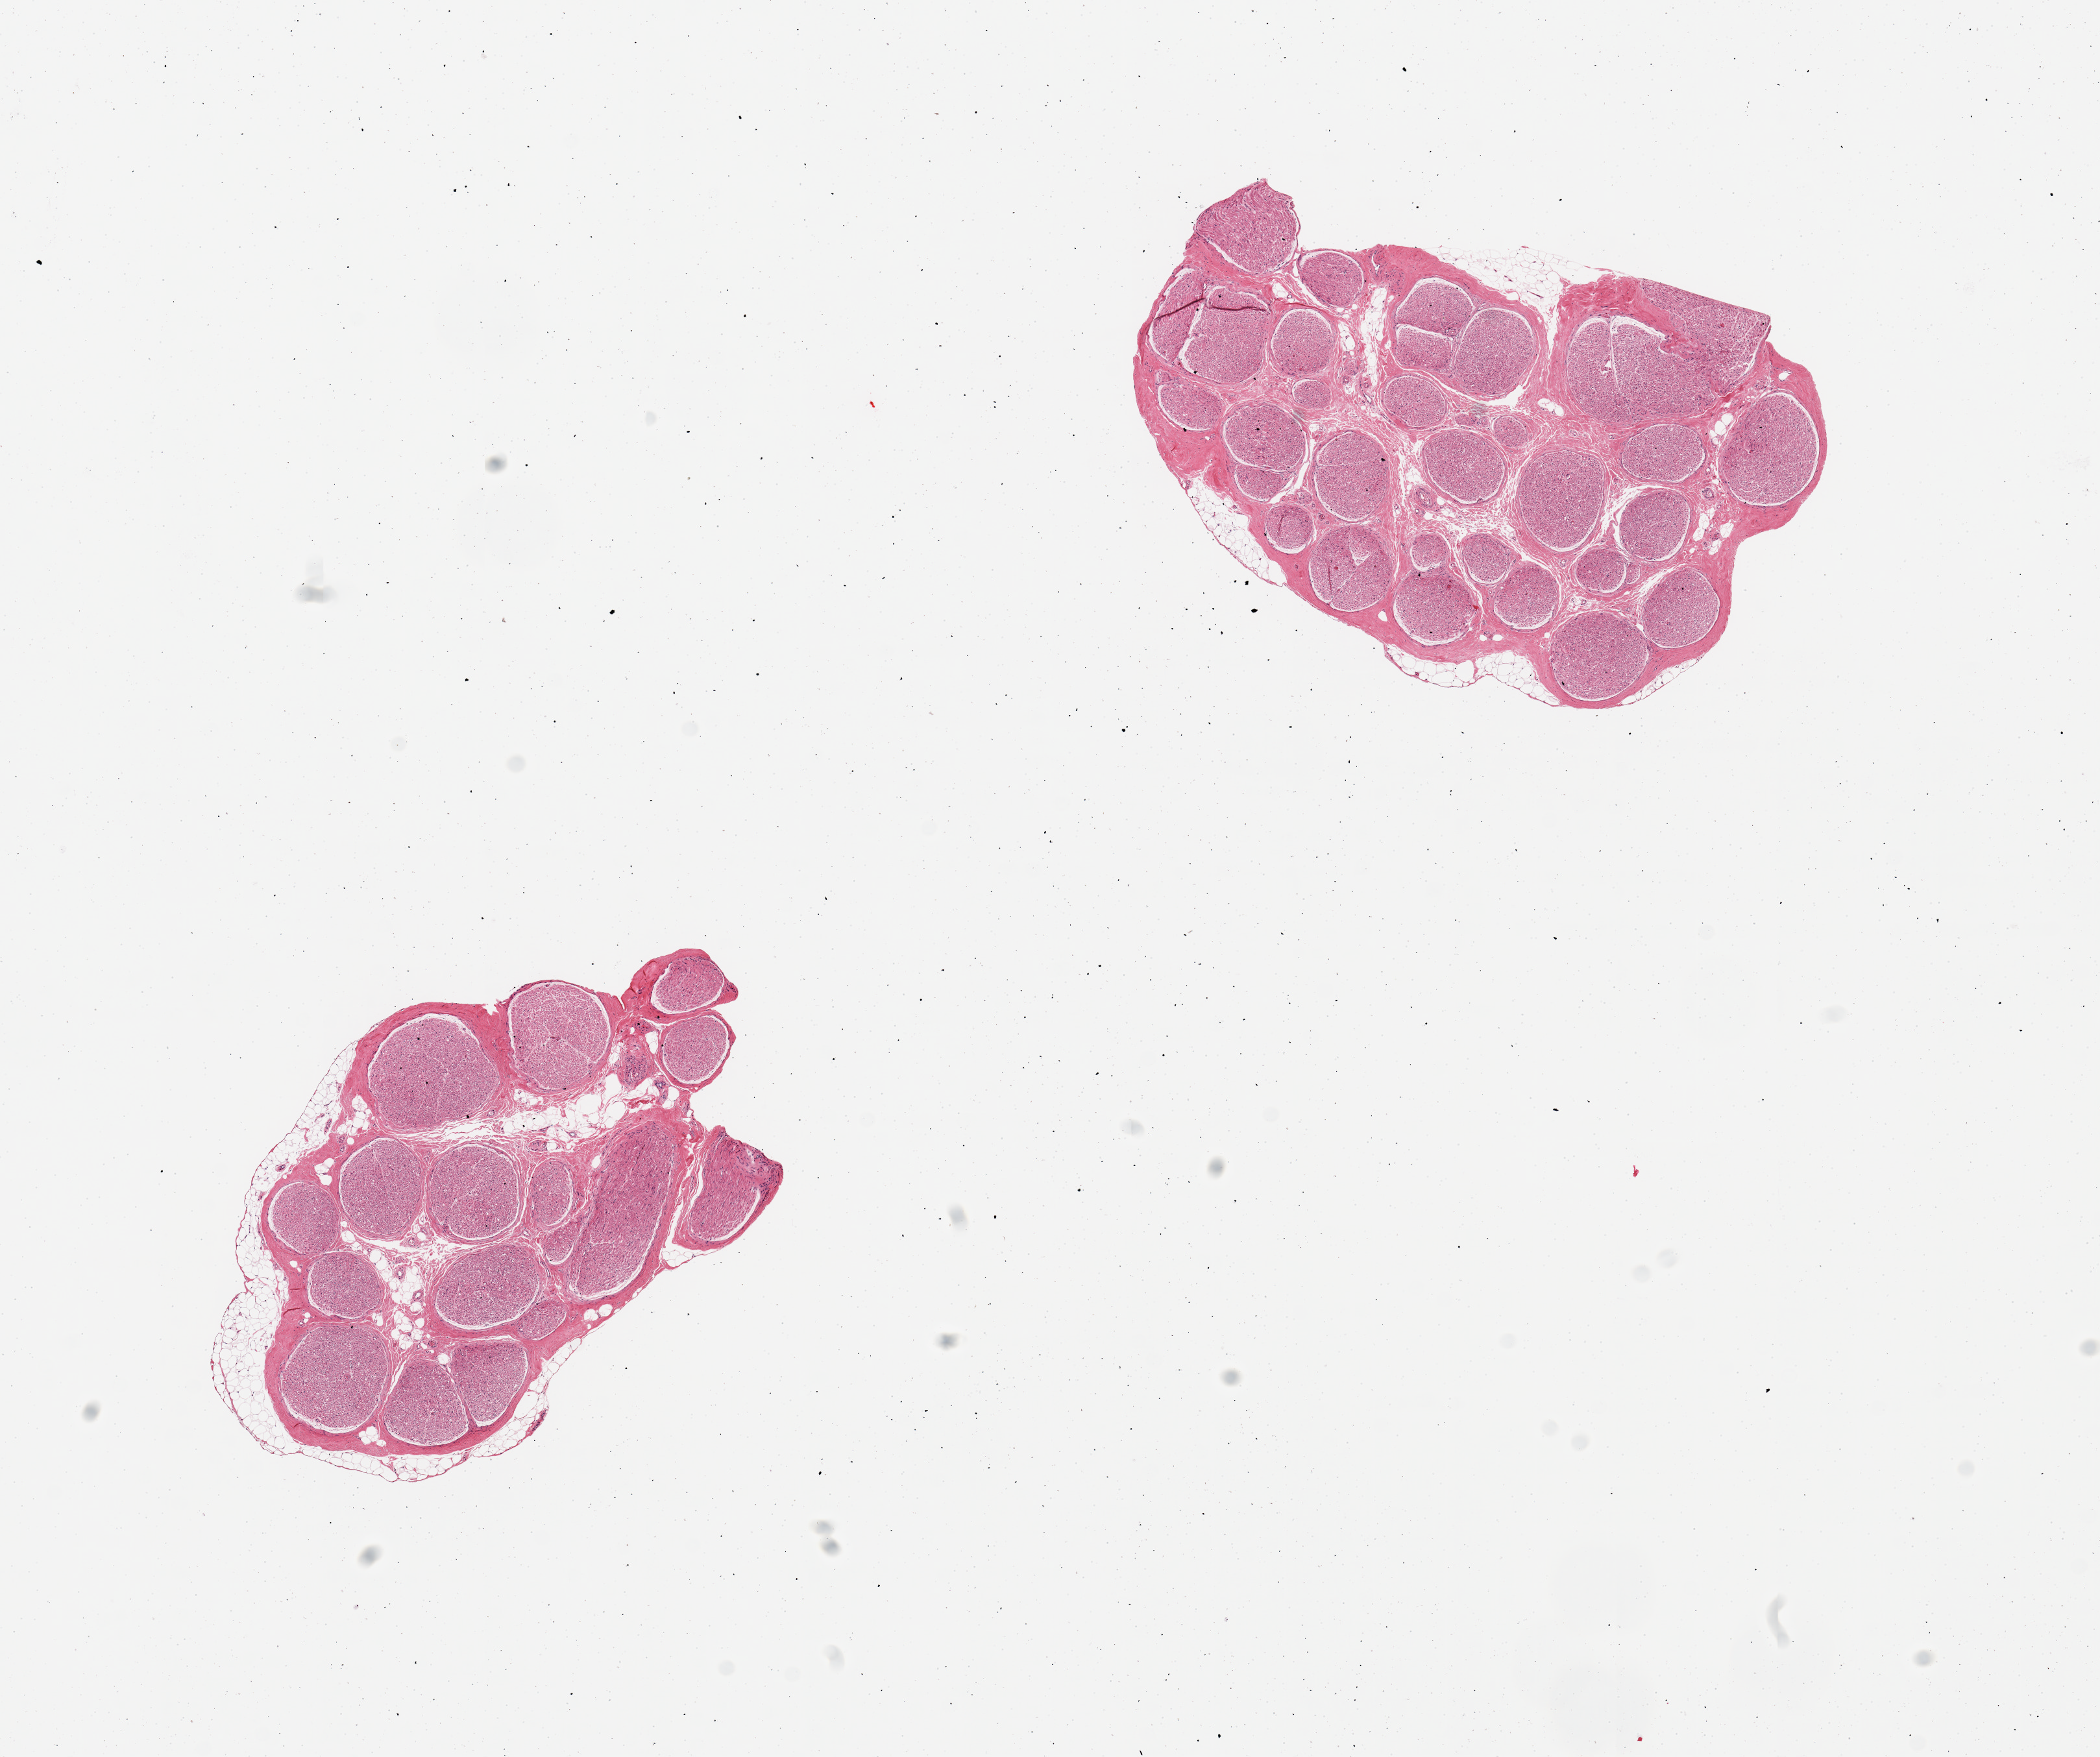
Haematoxylin and eosin whole-slide image — whole scanned area (about 12.8 x 10.7 mm, slide scanned at 20x) shown as a low-resolution overview; PAXgene-fixed paraffin-embedded (PFPE) section; section of tibial nerve (target tissue); donor tissue sample. Female donor.
- reviewer comment on this tissue sample: 2 pieces; 5% internal and external fat